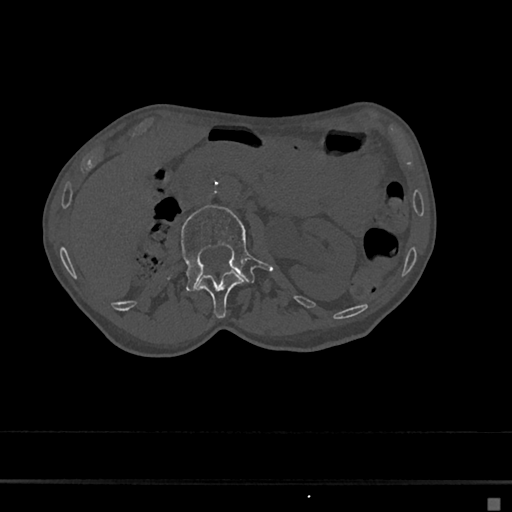
CT including the spine, one axial slice; position 34 of 797 along the scan axis; reconstruction kernel Br40s/3; 120 kVp; bone window (W 1800 / L 400 HU); 512 × 512 image matrix, field of view 360 × 360 mm. Female patient, age 68 years. From the clinical record (not read from this slice): primary cancer: renal.
Annotated regions visible in this slice (semi-automatic segmentation, software-assisted and operator-edited):
- L1 vertebra: bounding box (x1, y1, x2, y2) in pixels: (196, 270, 244, 319)
- L2 vertebra: (180, 205, 272, 291)